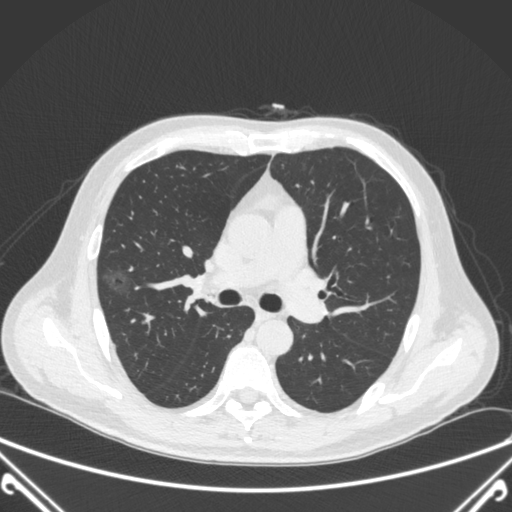
Chest CT, one axial slice; 120 kVp; lung window (W 1500 / L -600 HU); 1 mm slice thickness; 512 × 512 image matrix. Male patient, age 64 years. From the clinical record (not read from this slice): clinical TNM (as recorded): T1c N0 M0; histopathological grade: G2.
Structures marked on this image (rectangle marked by the reading radiologist):
- lung tumour (recorded histology: adenocarcinoma): bounding box <99,256,132,299> (left, top, right, bottom; pixels)